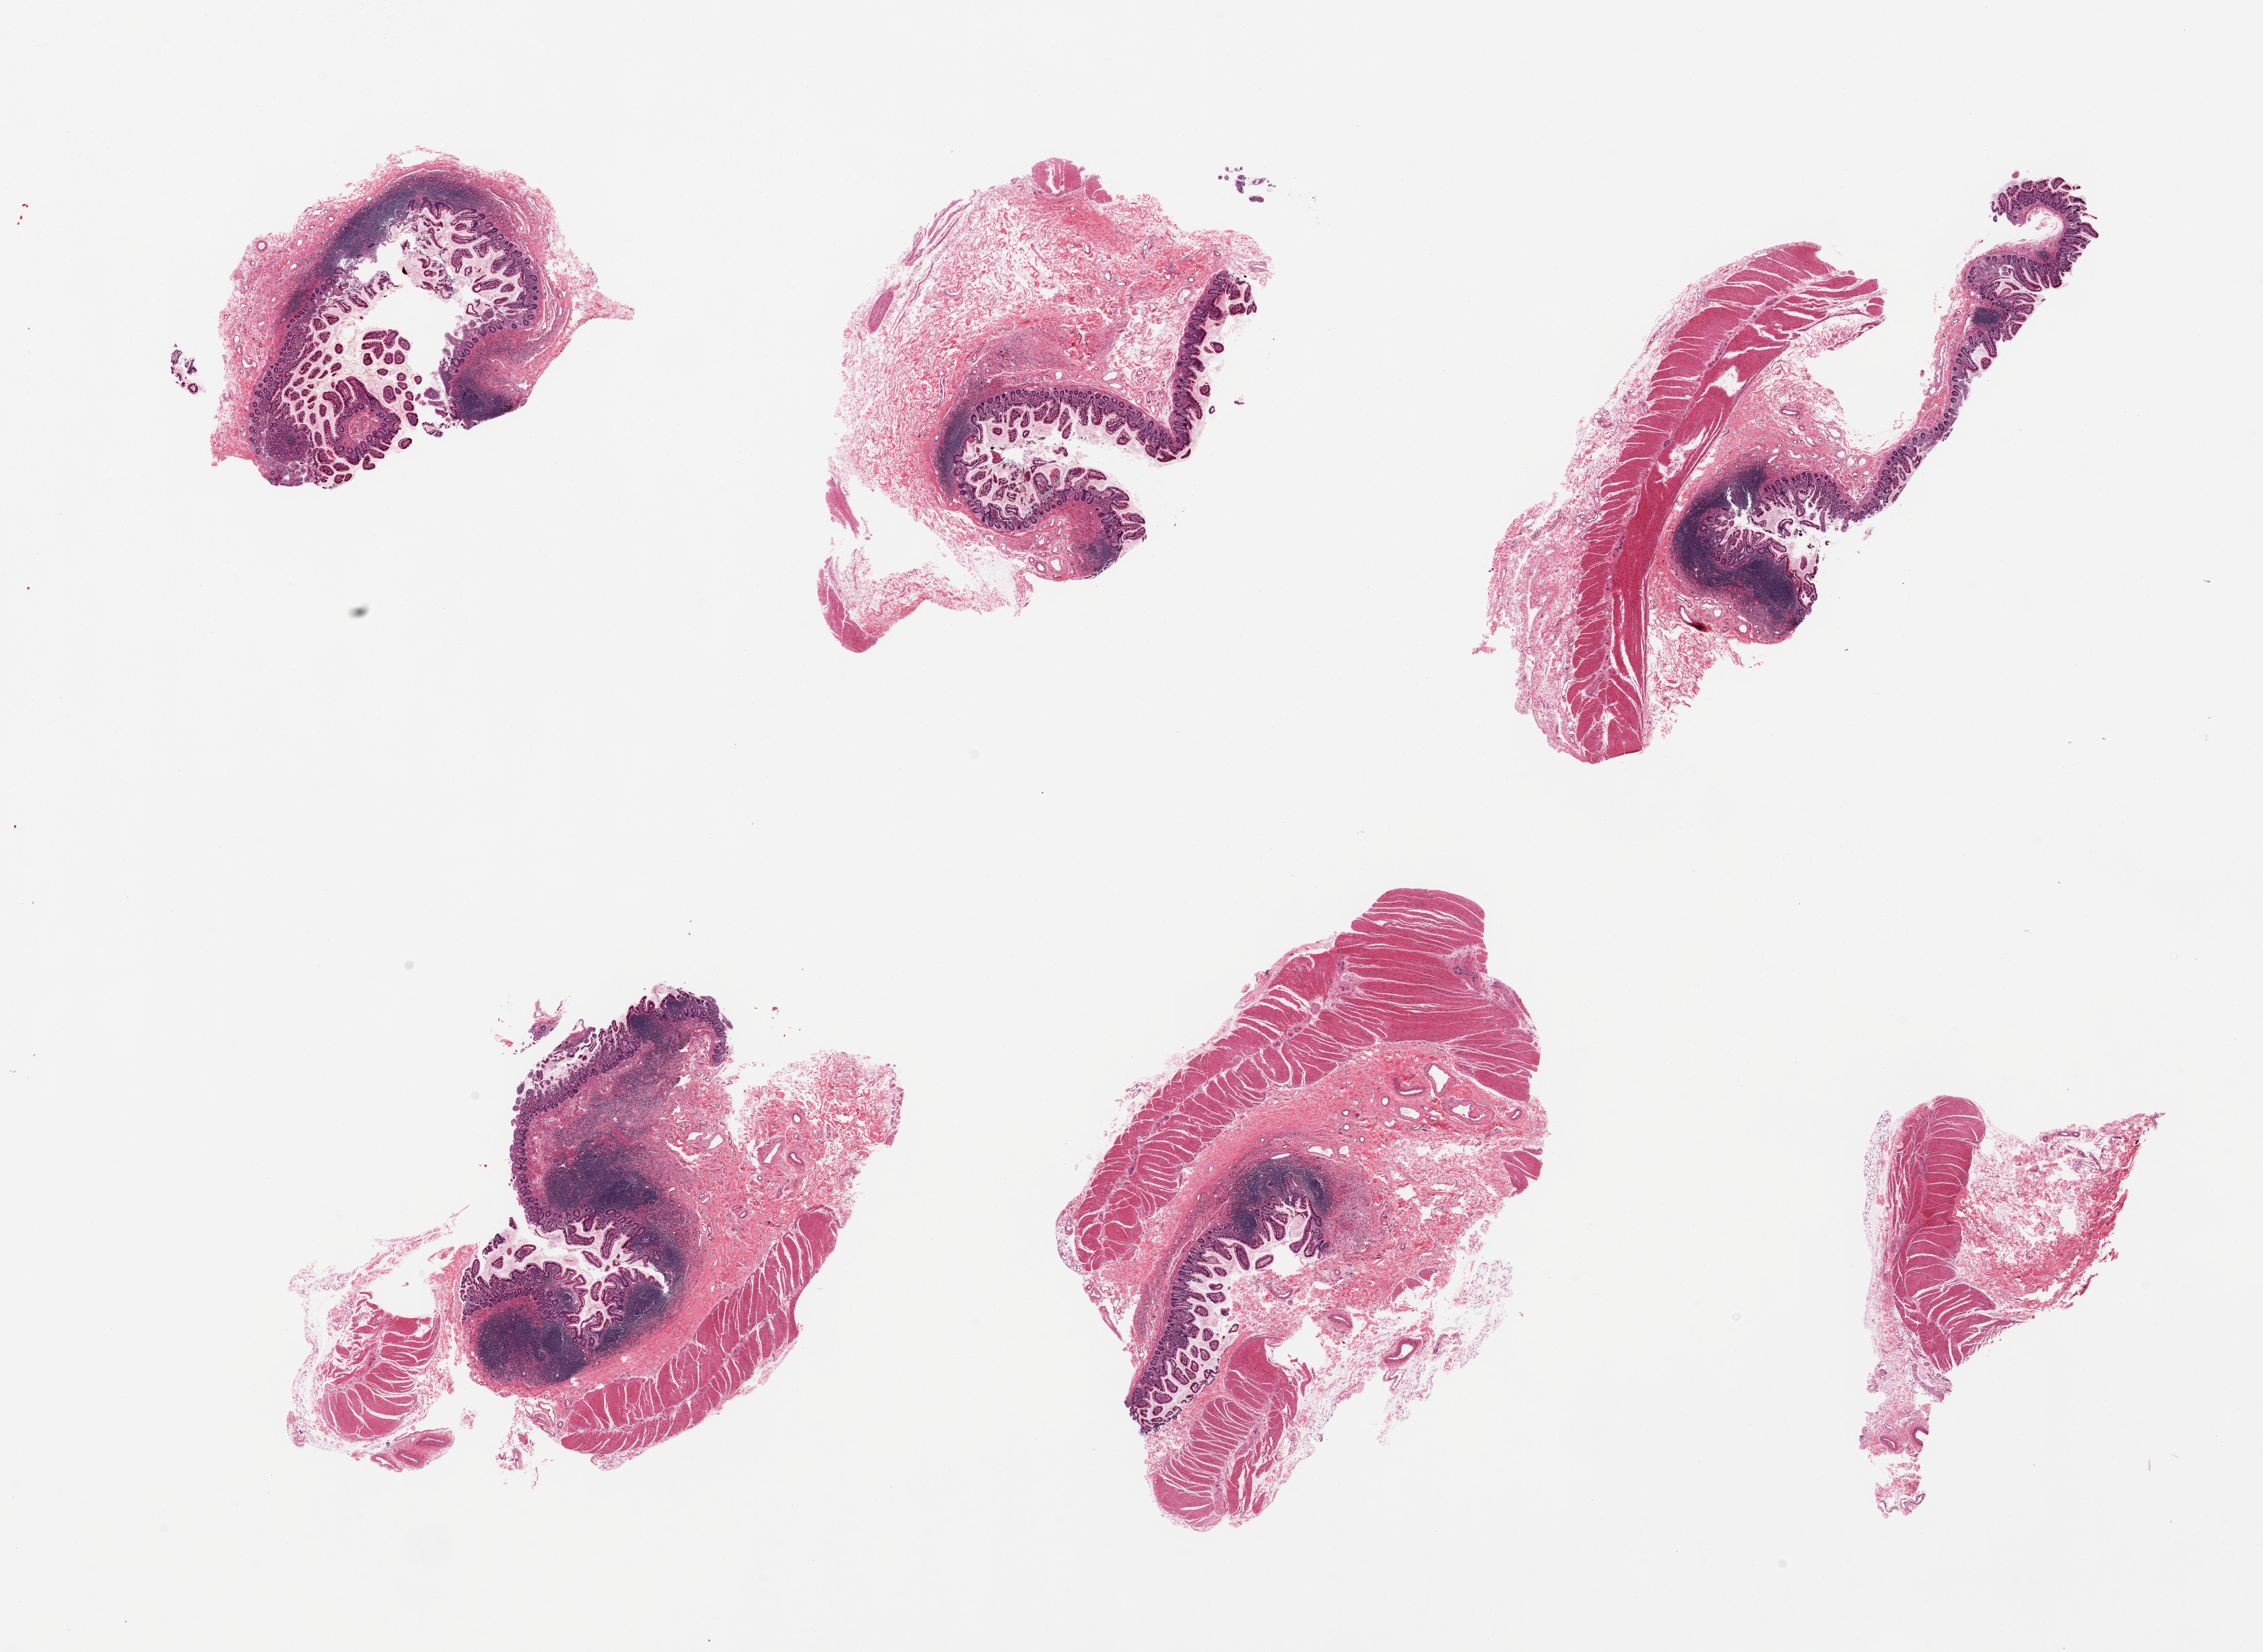
Digitized H&E-stained section, low-resolution overview of the scanned area, about 26.6 x 19.4 mm (from a 20x scan), PAXgene-fixed paraffin-embedded (PFPE) section, sampled site (target tissue): ileum, donor tissue sample.
Reviewer comment on this tissue sample: 6 pieces, 5 with lymphoid tissue.